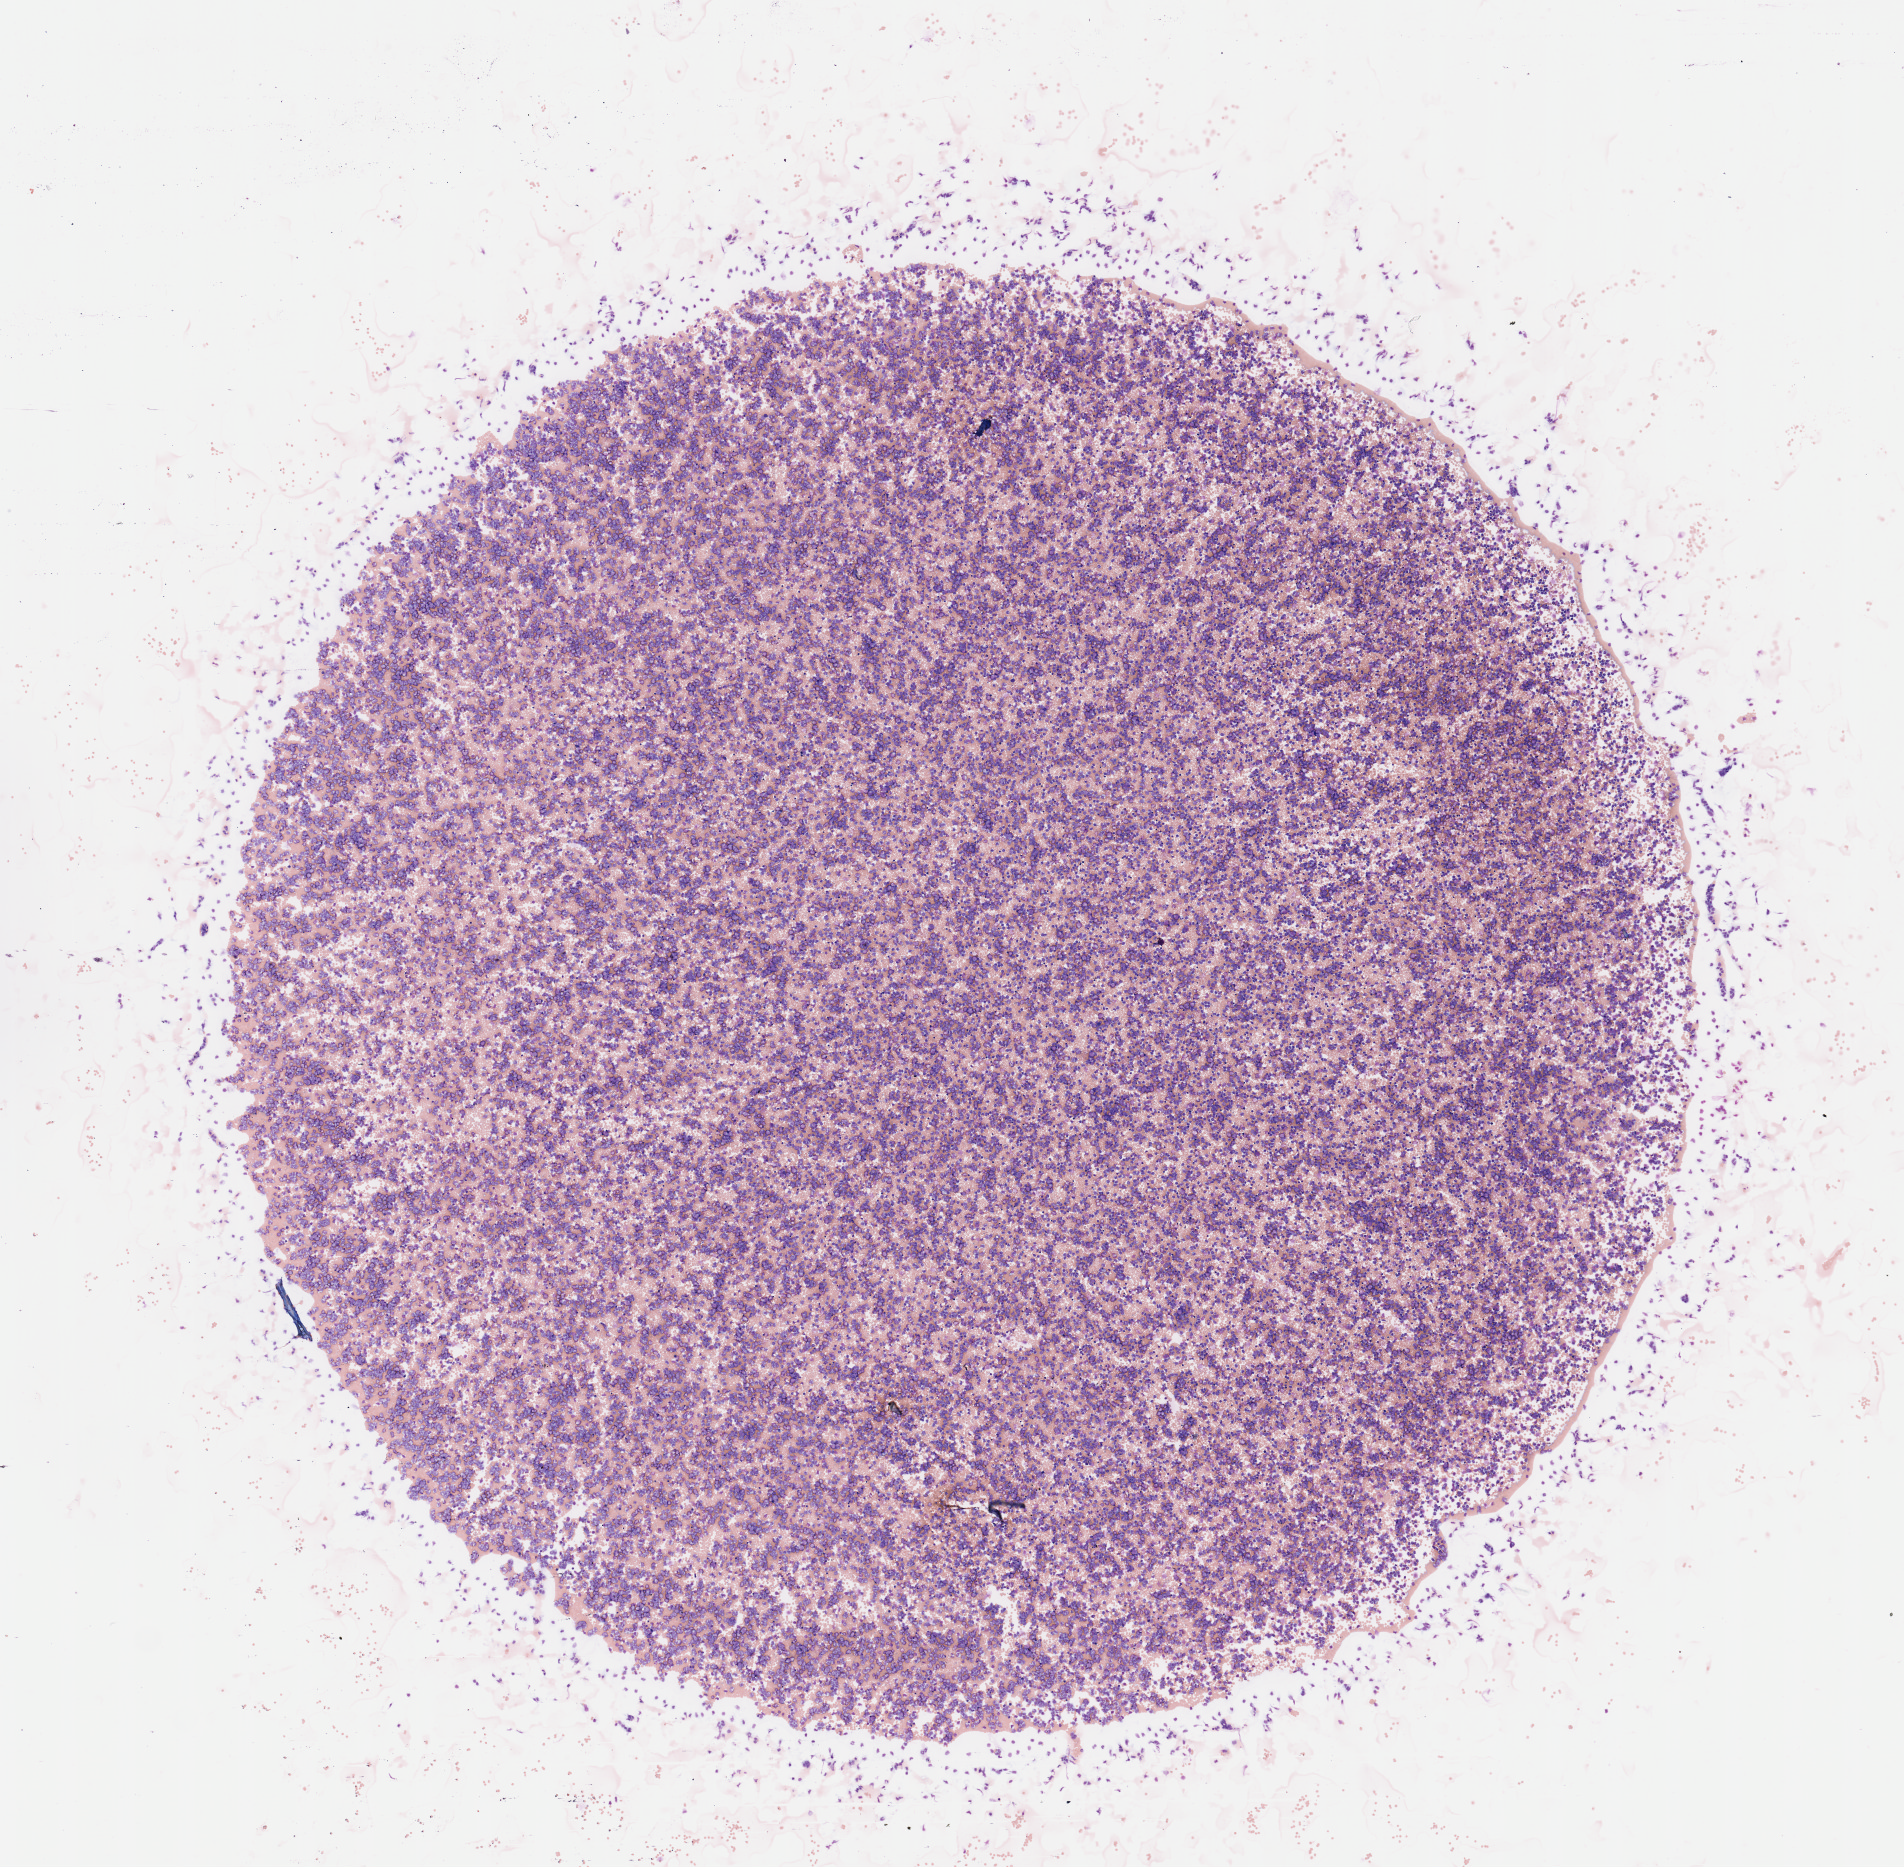
H&E-stained whole-slide image — whole scanned area (about 7.5 x 7.4 mm) shown as a low-resolution overview, peripheral blood (leukaemic) sample. Male, 60 y/o. Blasts: 20%.
Diagnosis: Acute Myeloid Leukemia. WHO classification: AML not otherwise specified.